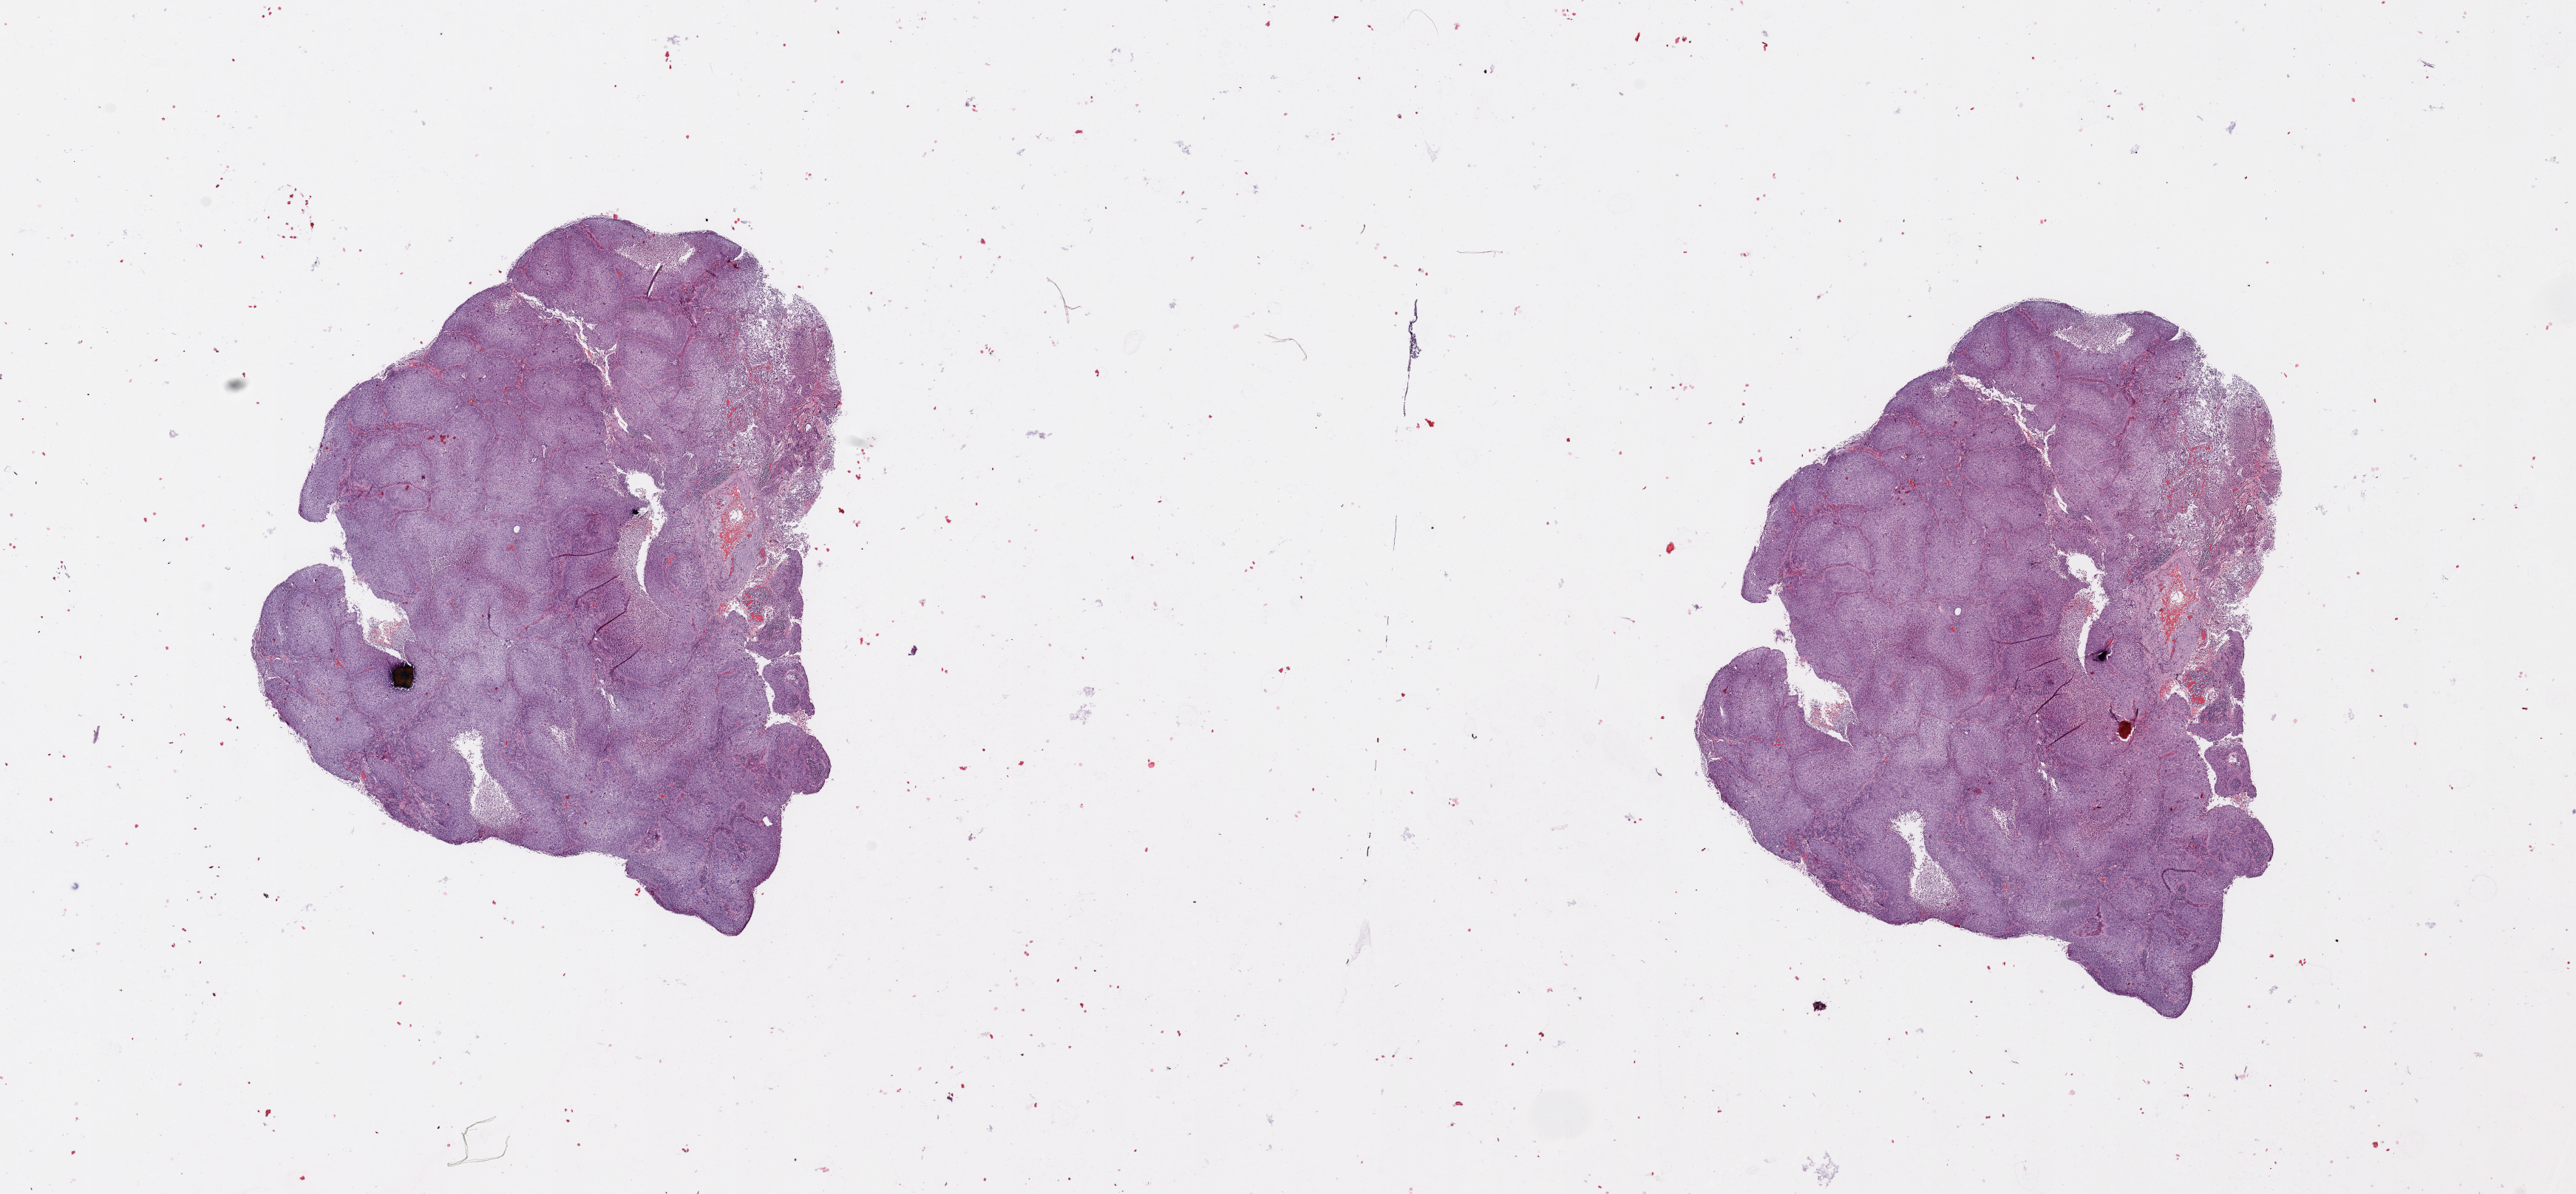
H&E whole-slide image, shown as a low-resolution overview of the whole scanned area (about 27.6 x 12.8 mm, from a 20x scan). Tumour tissue sample, lung. Patient: female, age 64 years. Histologic grade: G3 (poorly differentiated).
• primary tumour site (as recorded): right lower lobe
• histologic diagnosis: Squamous cell carcinoma, NOS
• AJCC pathologic stage: IA